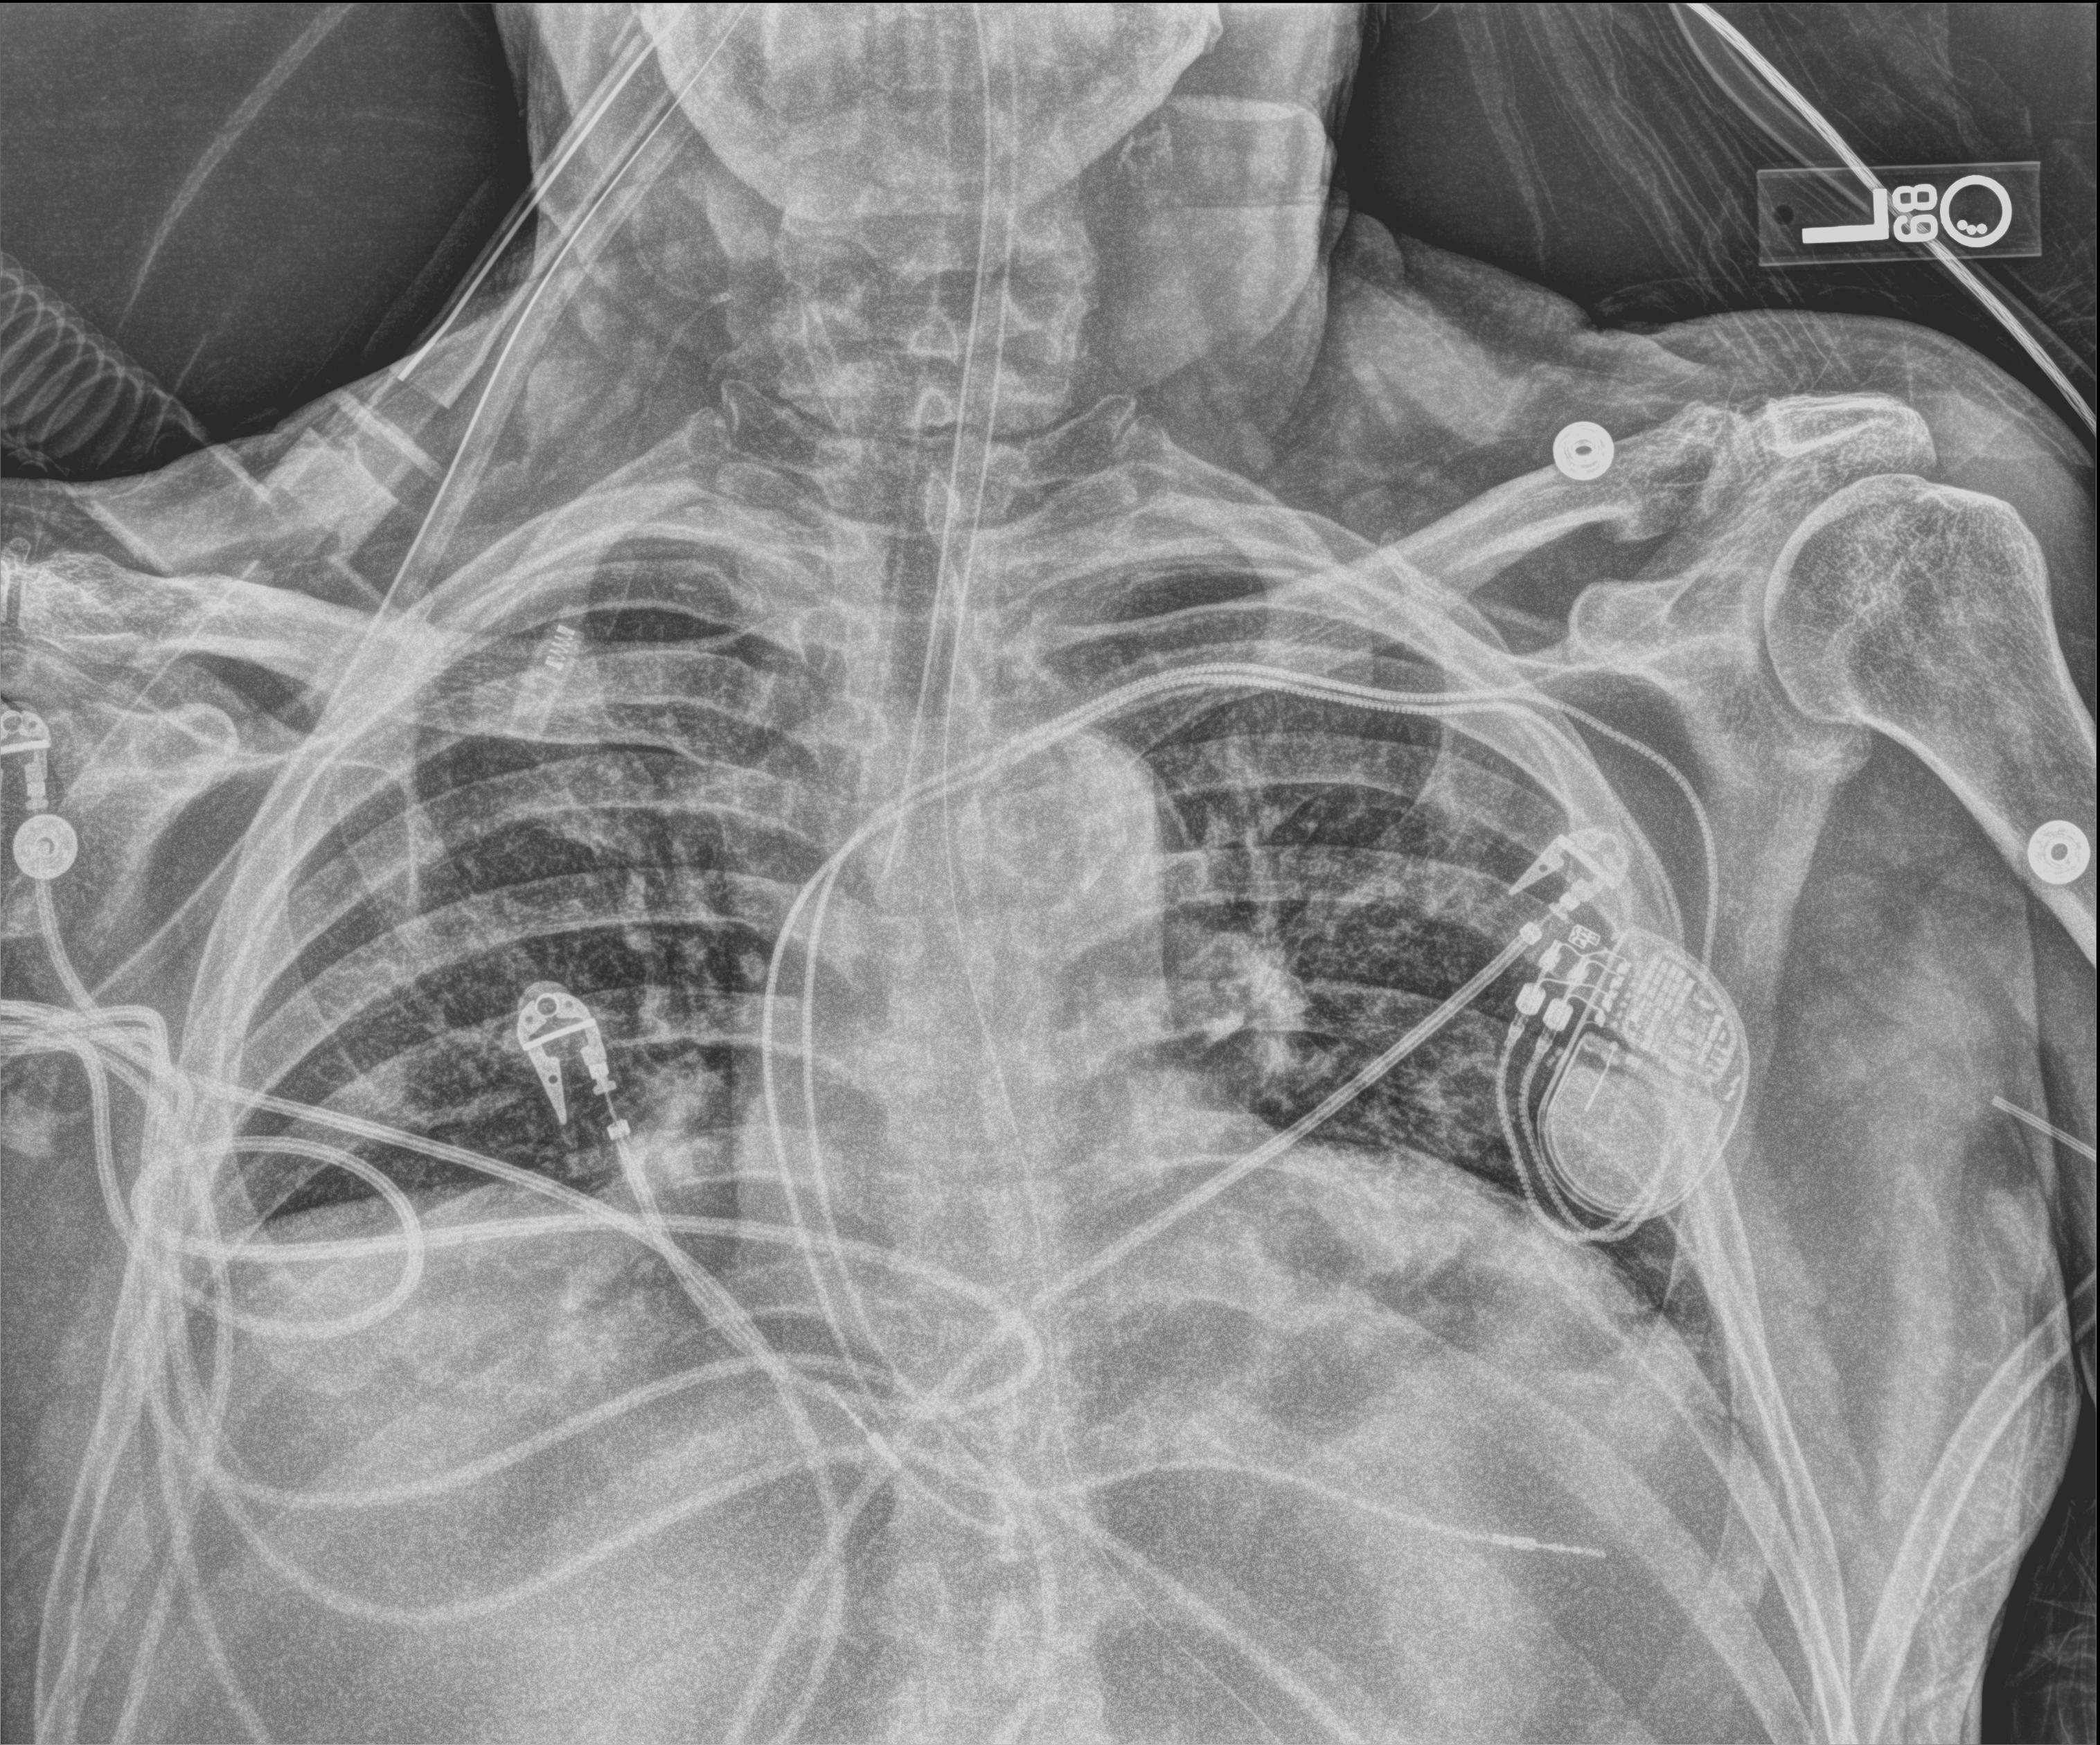
Bedside chest radiograph (digital radiography), anteroposterior (AP) projection. Patient hospitalised with COVID-19; male, aged 60–74 years.
Hospital-stay facts (about this admission, not read from this image; timing relative to this image not recorded): admitted to intensive care during this hospital stay: yes; length of hospital stay: 41 days.